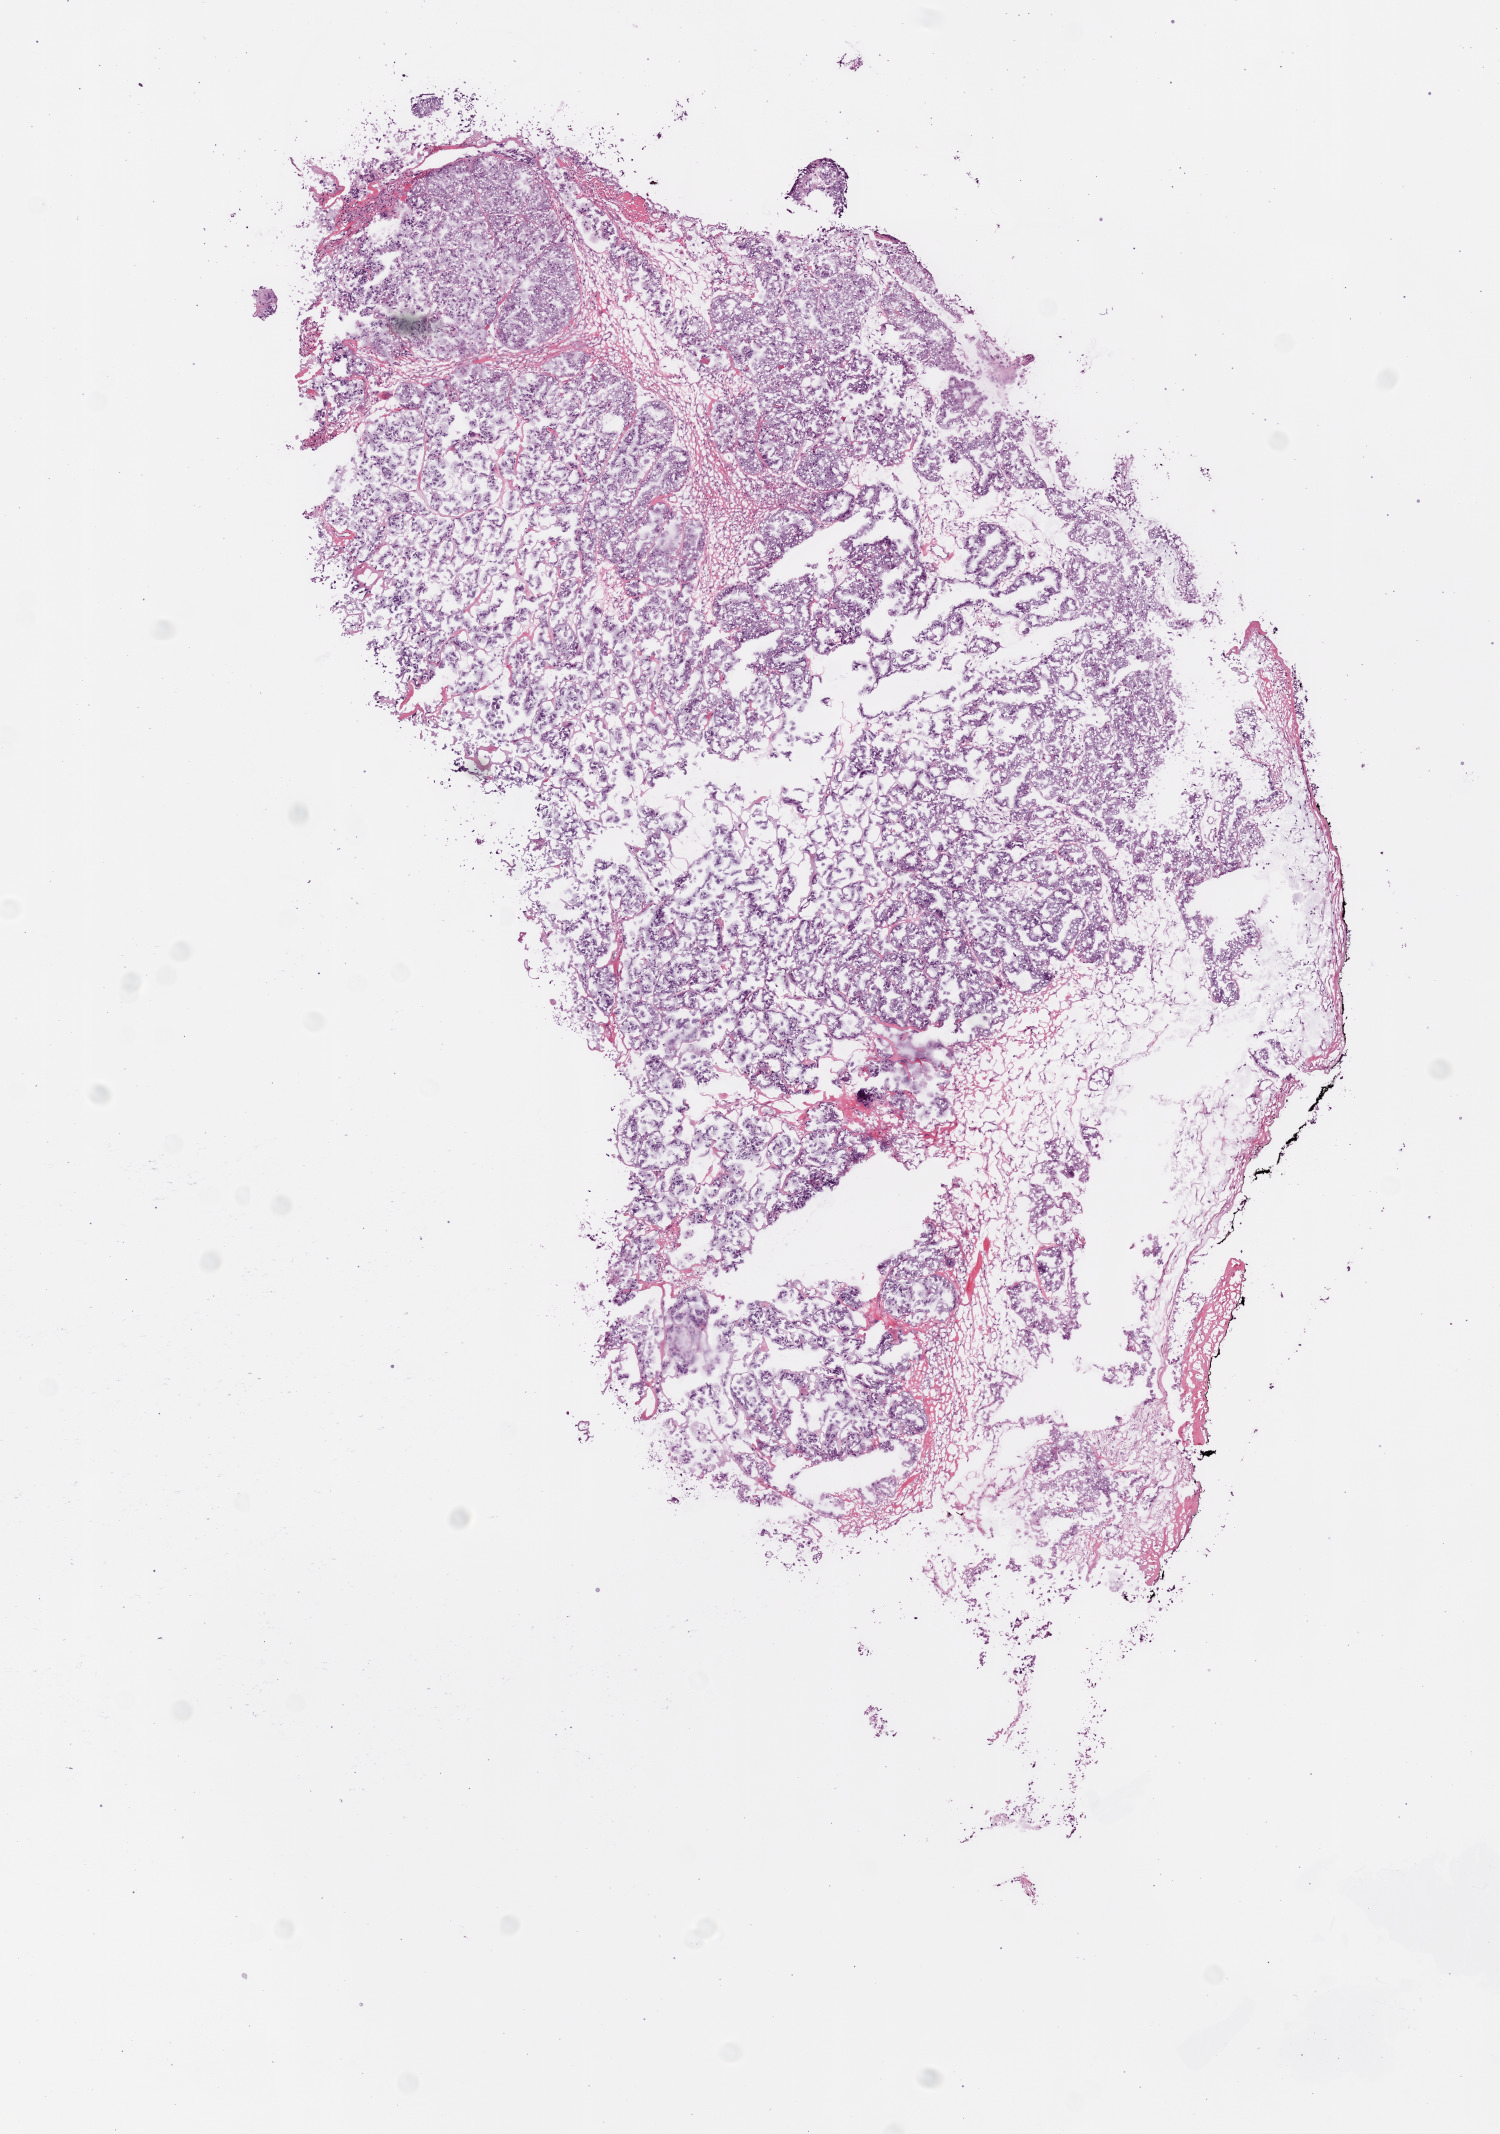
H&E whole-slide image — a low-resolution overview of the entire scanned area, about 6.0 x 8.6 mm (acquisition: 20x scan). Frozen section from the top of the tissue portion. Primary tumour sample from the ovary. Female patient; age at initial diagnosis 75 years. Histologic grade: G3 (poorly differentiated). Pathologist review of this section (percent, as recorded): tumour cells 75%, tumour nuclei 80%, normal cells 20%, stromal cells 0%, necrosis 5%.
FIGO stage: IIIC. Pathologic diagnosis: Serous cystadenocarcinoma, NOS.